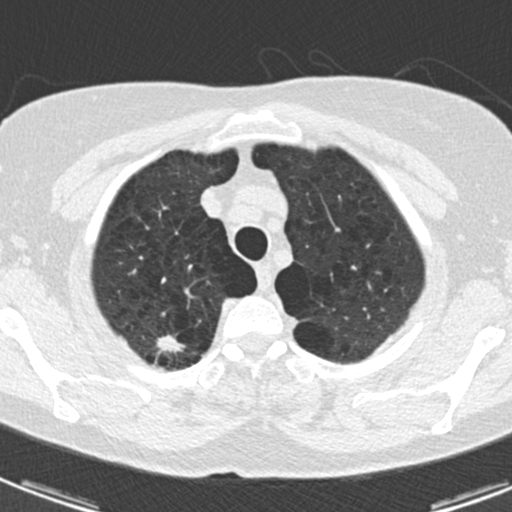
Low-dose screening chest CT, one axial slice; slice 152 of 174 in the series (ordered by position); reconstruction kernel B30f; lung window (W 1500 / L -600 HU); 2 mm slice thickness; 512 × 512 image matrix, field of view 281 × 281 mm.
Outlined on this slice (expert manual segmentation):
- lesion 1 (tumor, upper lobe of right lung): bounding box <157,334,185,352> (left, top, right, bottom; pixels)